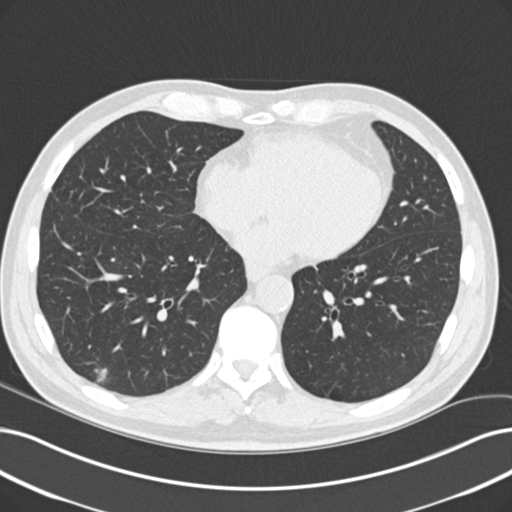
Chest CT (low-dose screening protocol), one axial image, baseline screening round, lung window (W 1500 / L -600 HU), 2 mm slice thickness, standard (soft-tissue) reconstruction kernel (B30f), slice 140 of 229 in the series, 512 × 512 image matrix. Male participant, aged 60 years at enrolment. Former smoker at enrolment.
- Lesion marked by an expert reader, bounding box <75,356,116,402> (left, top, right, bottom; pixels).
- The screening reader recorded 2 non-calcified nodules or masses ≥4 mm on this exam (right lower lobe, left lower lobe); which of them this box marks is not recorded.
- Later outcome: lung cancer diagnosed 64 days after this screen — acinar cell carcinoma, right lower lobe, moderately differentiated (G2), stage IA (AJCC 6th edition), 16 mm at pathology.